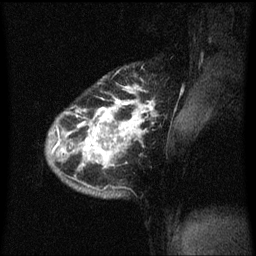
Breast MRI (dynamic contrast-enhanced), one sagittal slice; slice 50 of 60 in the series (ordered by position); dynamic contrast-enhanced series, image 2 of 3 at this slice position (ordered by acquisition); 1.5 T; TE 4.2 ms, TR 8.4 ms; 256 × 256 image matrix, field of view 200 × 200 mm. Female patient, age 34 years. Case-level facts recorded for this patient, not image findings: setting: breast cancer imaged before/during neoadjuvant chemotherapy; receptor status: HR-positive, HER2-negative.
Annotated regions visible in this slice (semi-automatic segmentation, software-assisted and operator-edited):
- analysis volume of interest (the breast-tissue region the enhancement analysis was run in; not a lesion): bounding box (x1, y1, x2, y2) in pixels: (46, 64, 159, 199)
- tumour enhancement mask (voxels above the 70 % enhancement threshold inside the analysis volume of interest): (52, 86, 155, 167)